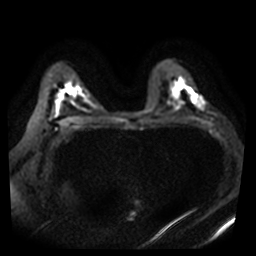
Breast MRI, one axial slice. Position 28 of 40 along the scan axis. Diffusion-weighted series; image 2 of 4 stored at this slice position (different b-values; order by instance number). 3 T. 5 mm slice thickness. 256 × 256 image matrix, field of view 360 × 360 mm. Female patient.
Structures marked on this image (outlined manually by an expert reader):
- tumour on diffusion-weighted imaging: bounding box [x1, y1, x2, y2] px = [201, 101, 205, 104]